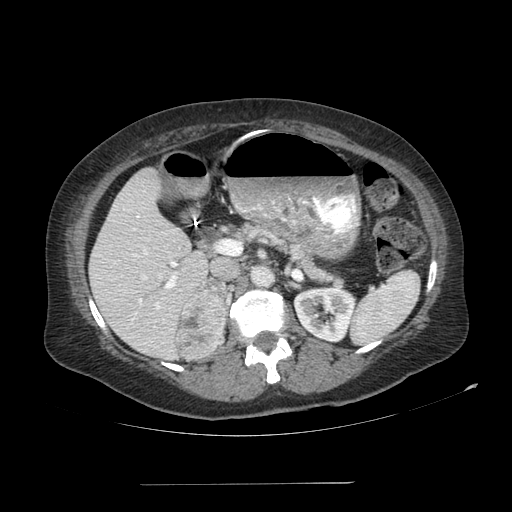
Contrast-enhanced abdominal CT, one axial slice; slice 59 of 113 in the series (ordered by position); reconstruction kernel SOFT; soft-tissue window (W 400 / L 40 HU); 2.5 mm slice thickness; 512 × 512 image matrix, field of view 440 × 440 mm. Patient: female, 67 years. Case-level facts recorded for this patient, not image findings: diagnosis: adrenocortical carcinoma; tumour side: right adrenal; tumour size at pathology: 9.8 cm; Ki-67 index: 59 %; stage (as recorded): 4.
Annotated regions visible in this slice (semi-automatic segmentation, software-assisted and operator-edited):
- mass: box from (x=177, y=280) to (x=226, y=358) px